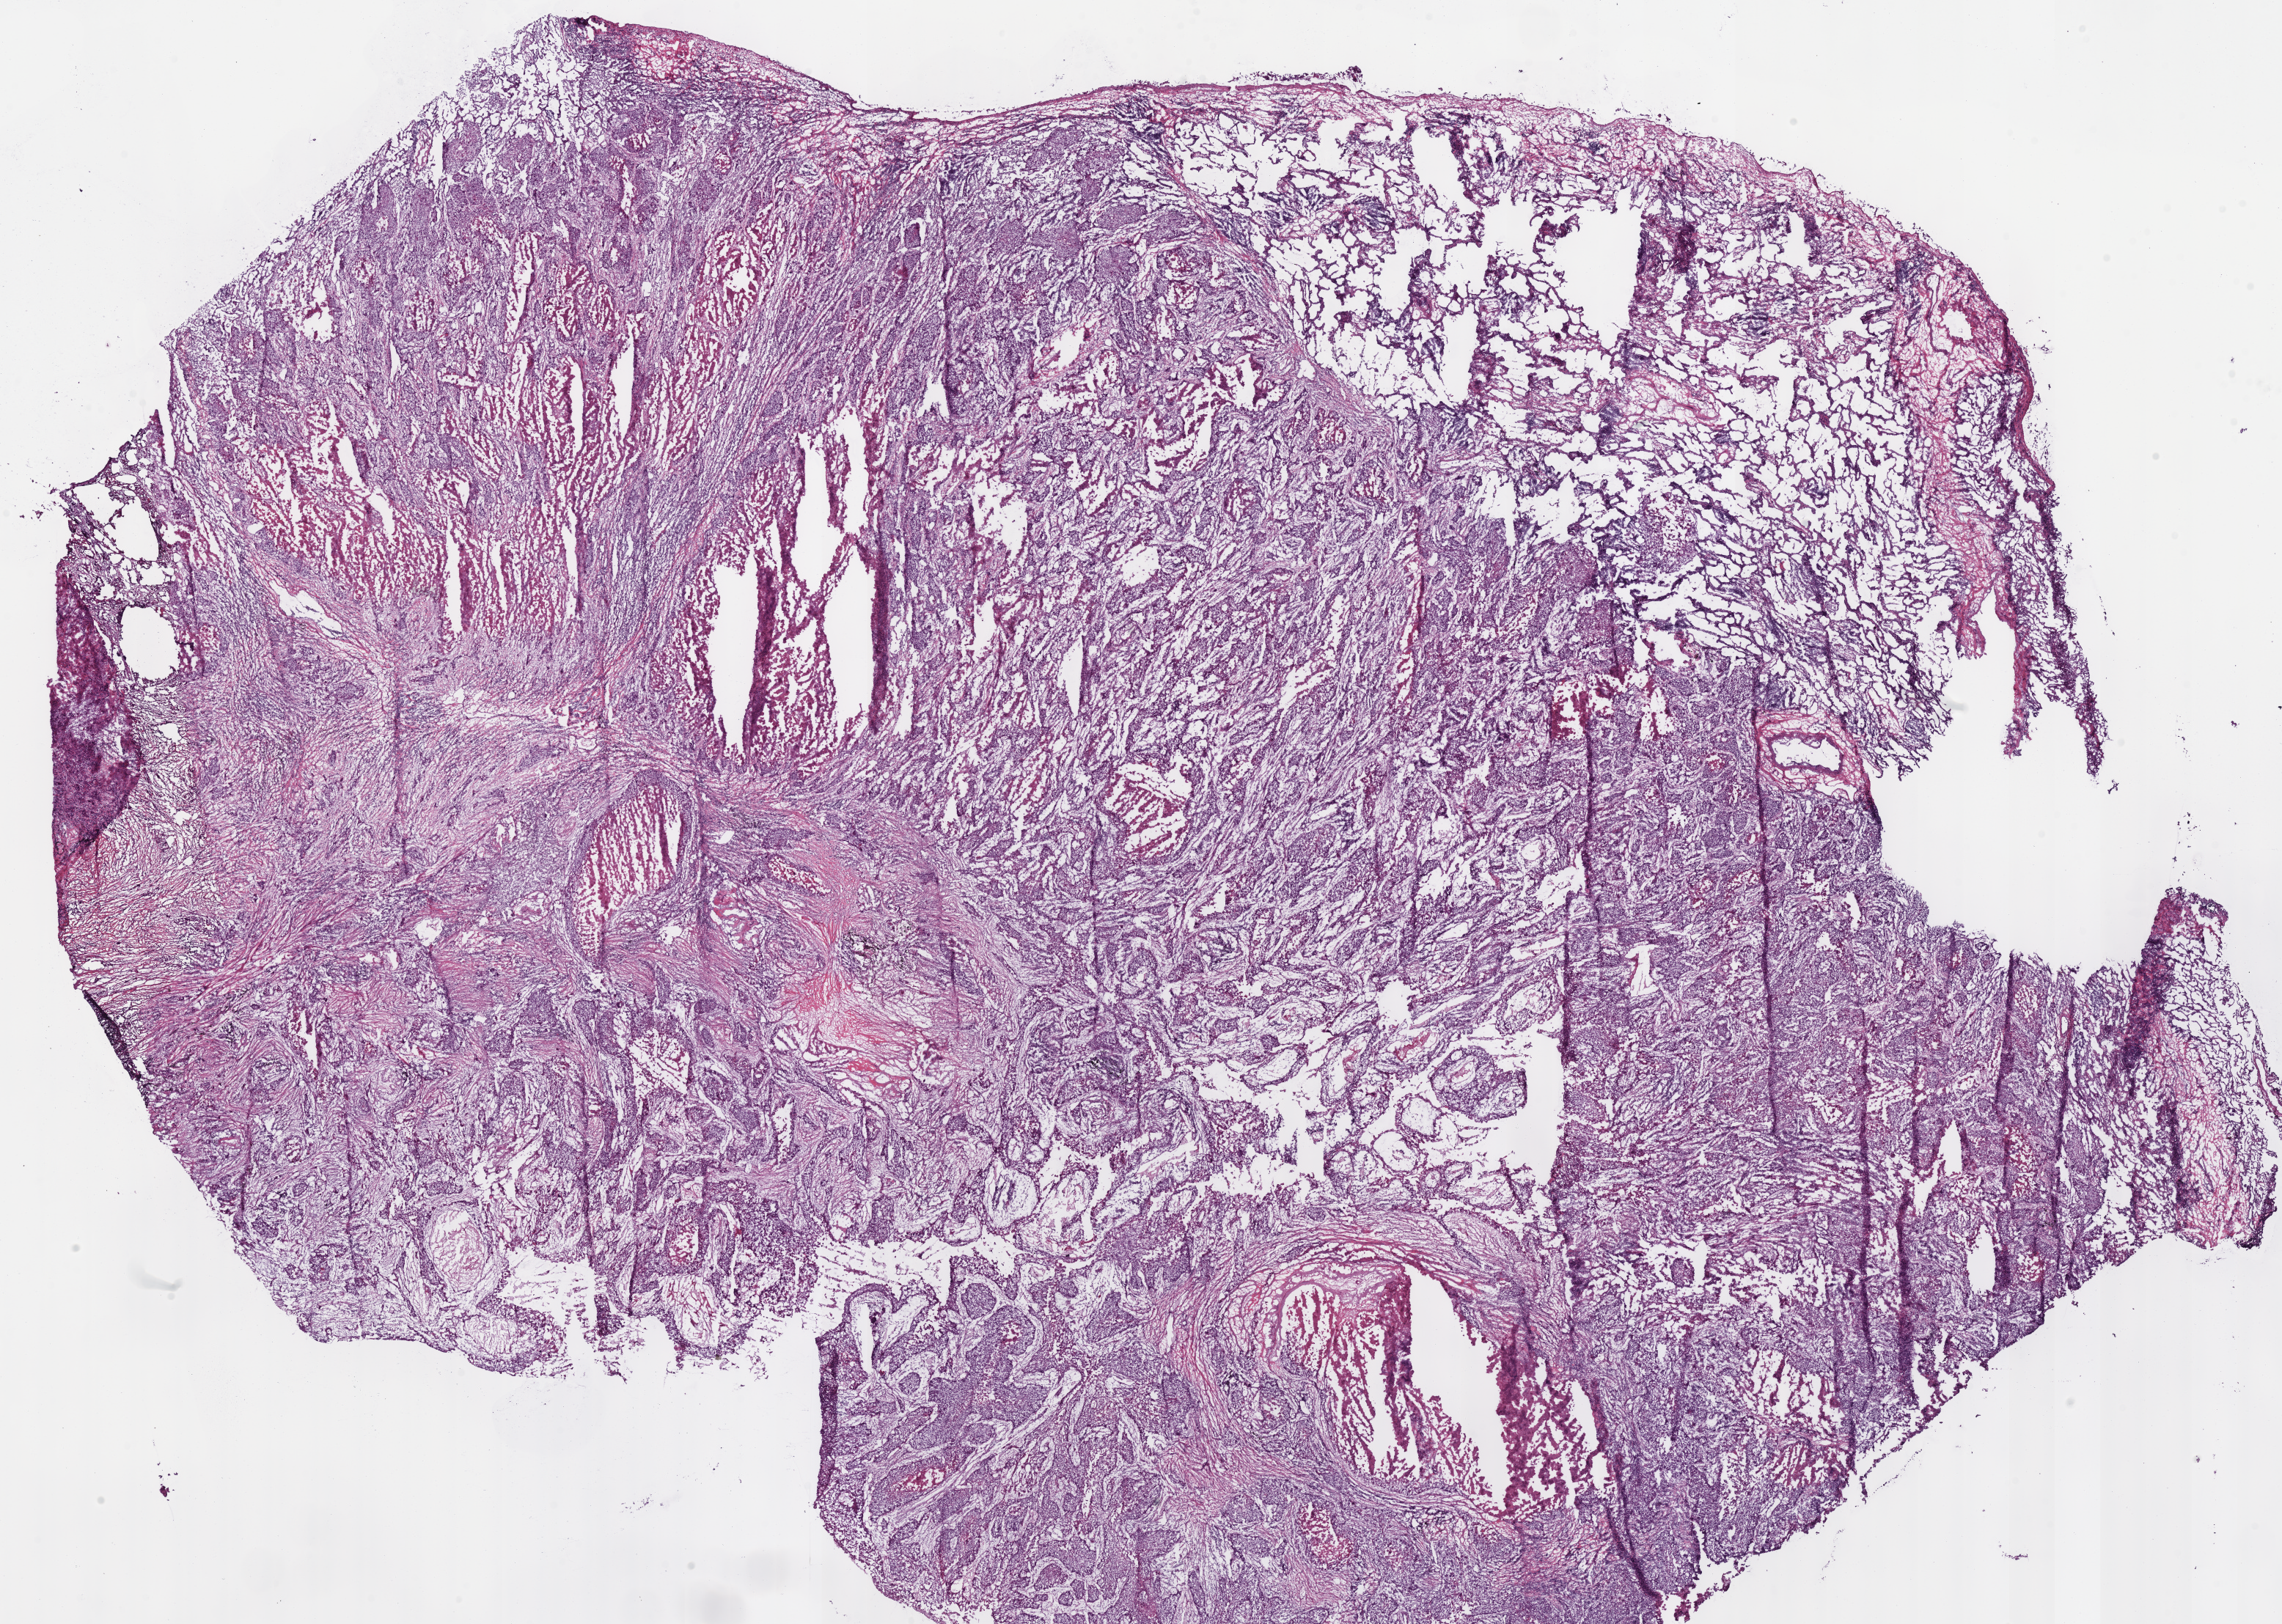
Hematoxylin and eosin (H&E) stained whole-slide image — low-resolution overview of the scanned area, about 24.5 x 17.4 mm; frozen section; lung, primary tumour sample. Male patient; age at initial diagnosis 72 years. Slide review estimates, as recorded: tumour cells 55%, tumour nuclei 60%, normal cells 15%, stromal cells 10%, necrosis 20%.
- laterality: right
- AJCC pathologic stage: IIIA (7th edition)
- diagnosis: Squamous cell carcinoma, NOS (lower lobe, lung)